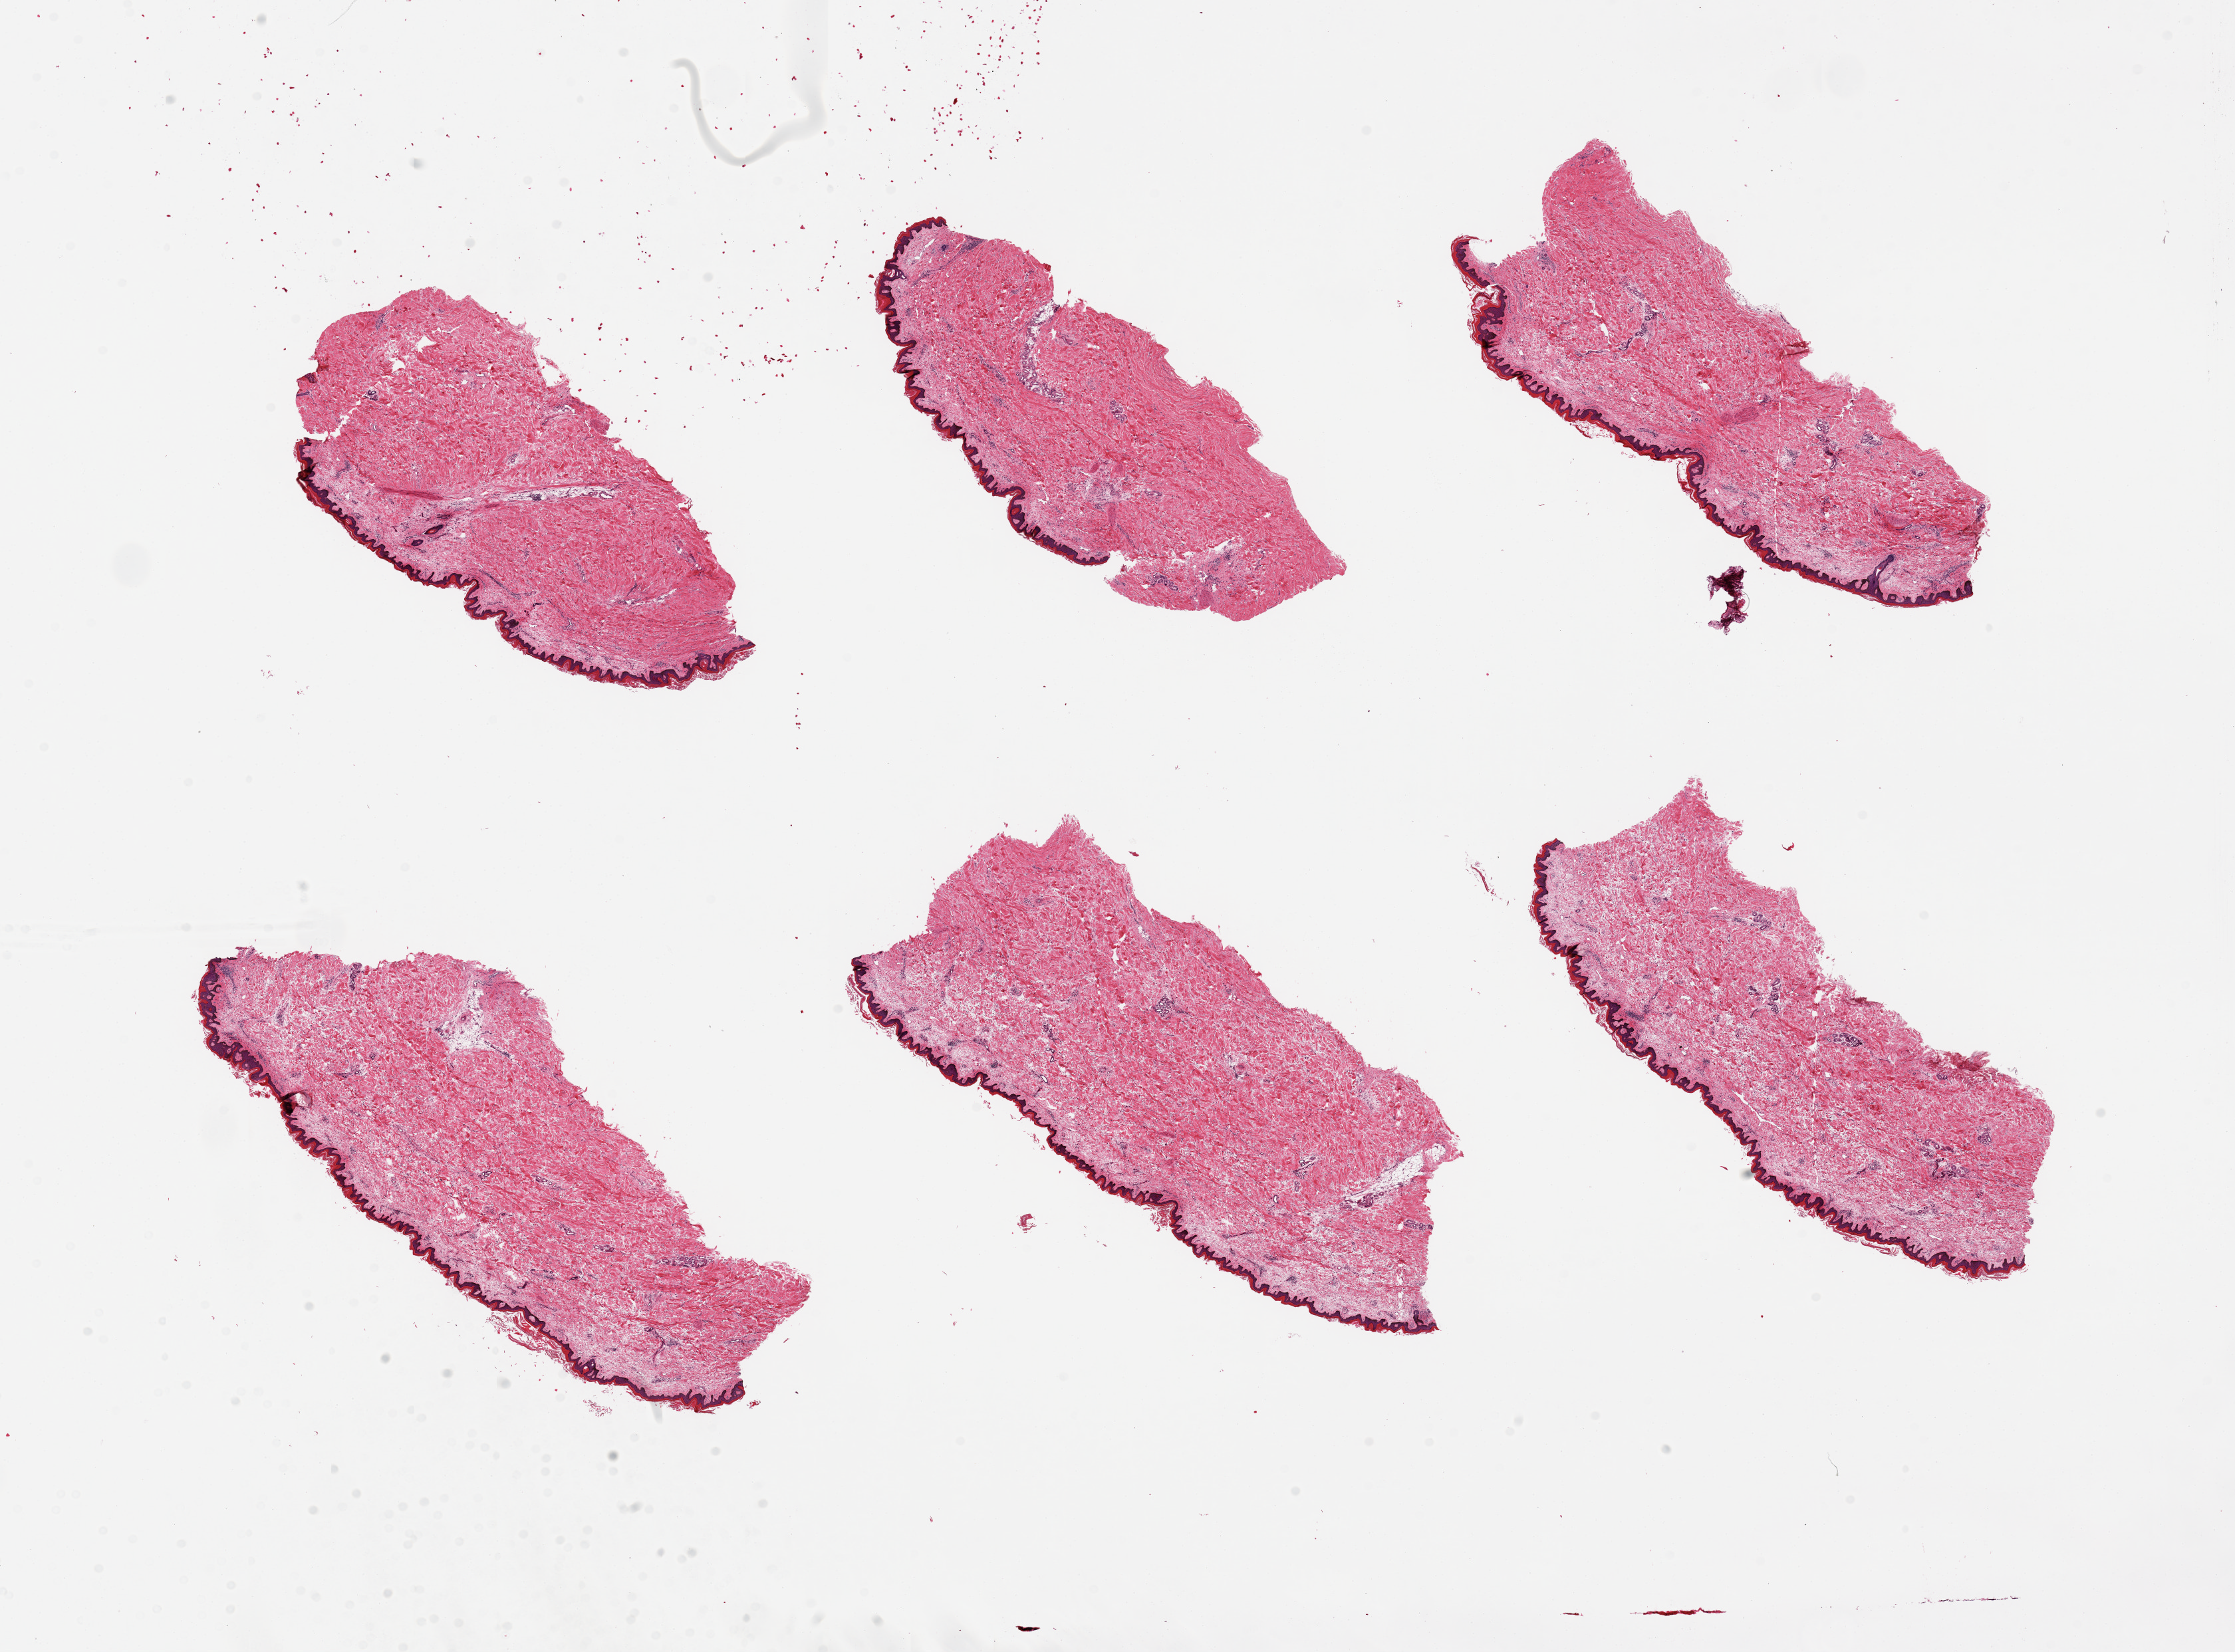
Hematoxylin and eosin (H&E) whole-slide image, low-resolution overview of the scanned area, about 26.6 x 19.7 mm (slide scanned at 20x). PAXgene-fixed paraffin-embedded (PFPE) section. Target tissue: skin of lower leg. Tissue donor sample.
Pathologist's review note for this sample: 6 pieces, up to 8x4mm; squamous epithelium ~1%thickness.